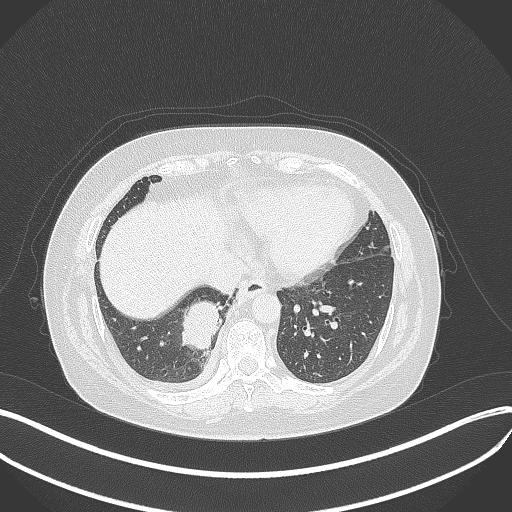
Chest CT, one axial slice; slice 106 of 381 in the series (ordered by position); lung window (W 1500 / L -600 HU); 1 mm slice thickness; 512 × 512 image matrix. Patient: female, 56 years. Case-level facts recorded for this patient, not image findings: clinical TNM (as recorded): T2b N1 M0.
Structures marked on this image (bounding box drawn by a radiologist):
- lung tumour (recorded histology: small cell carcinoma): bounding box [x1, y1, x2, y2] px = [180, 296, 223, 354]